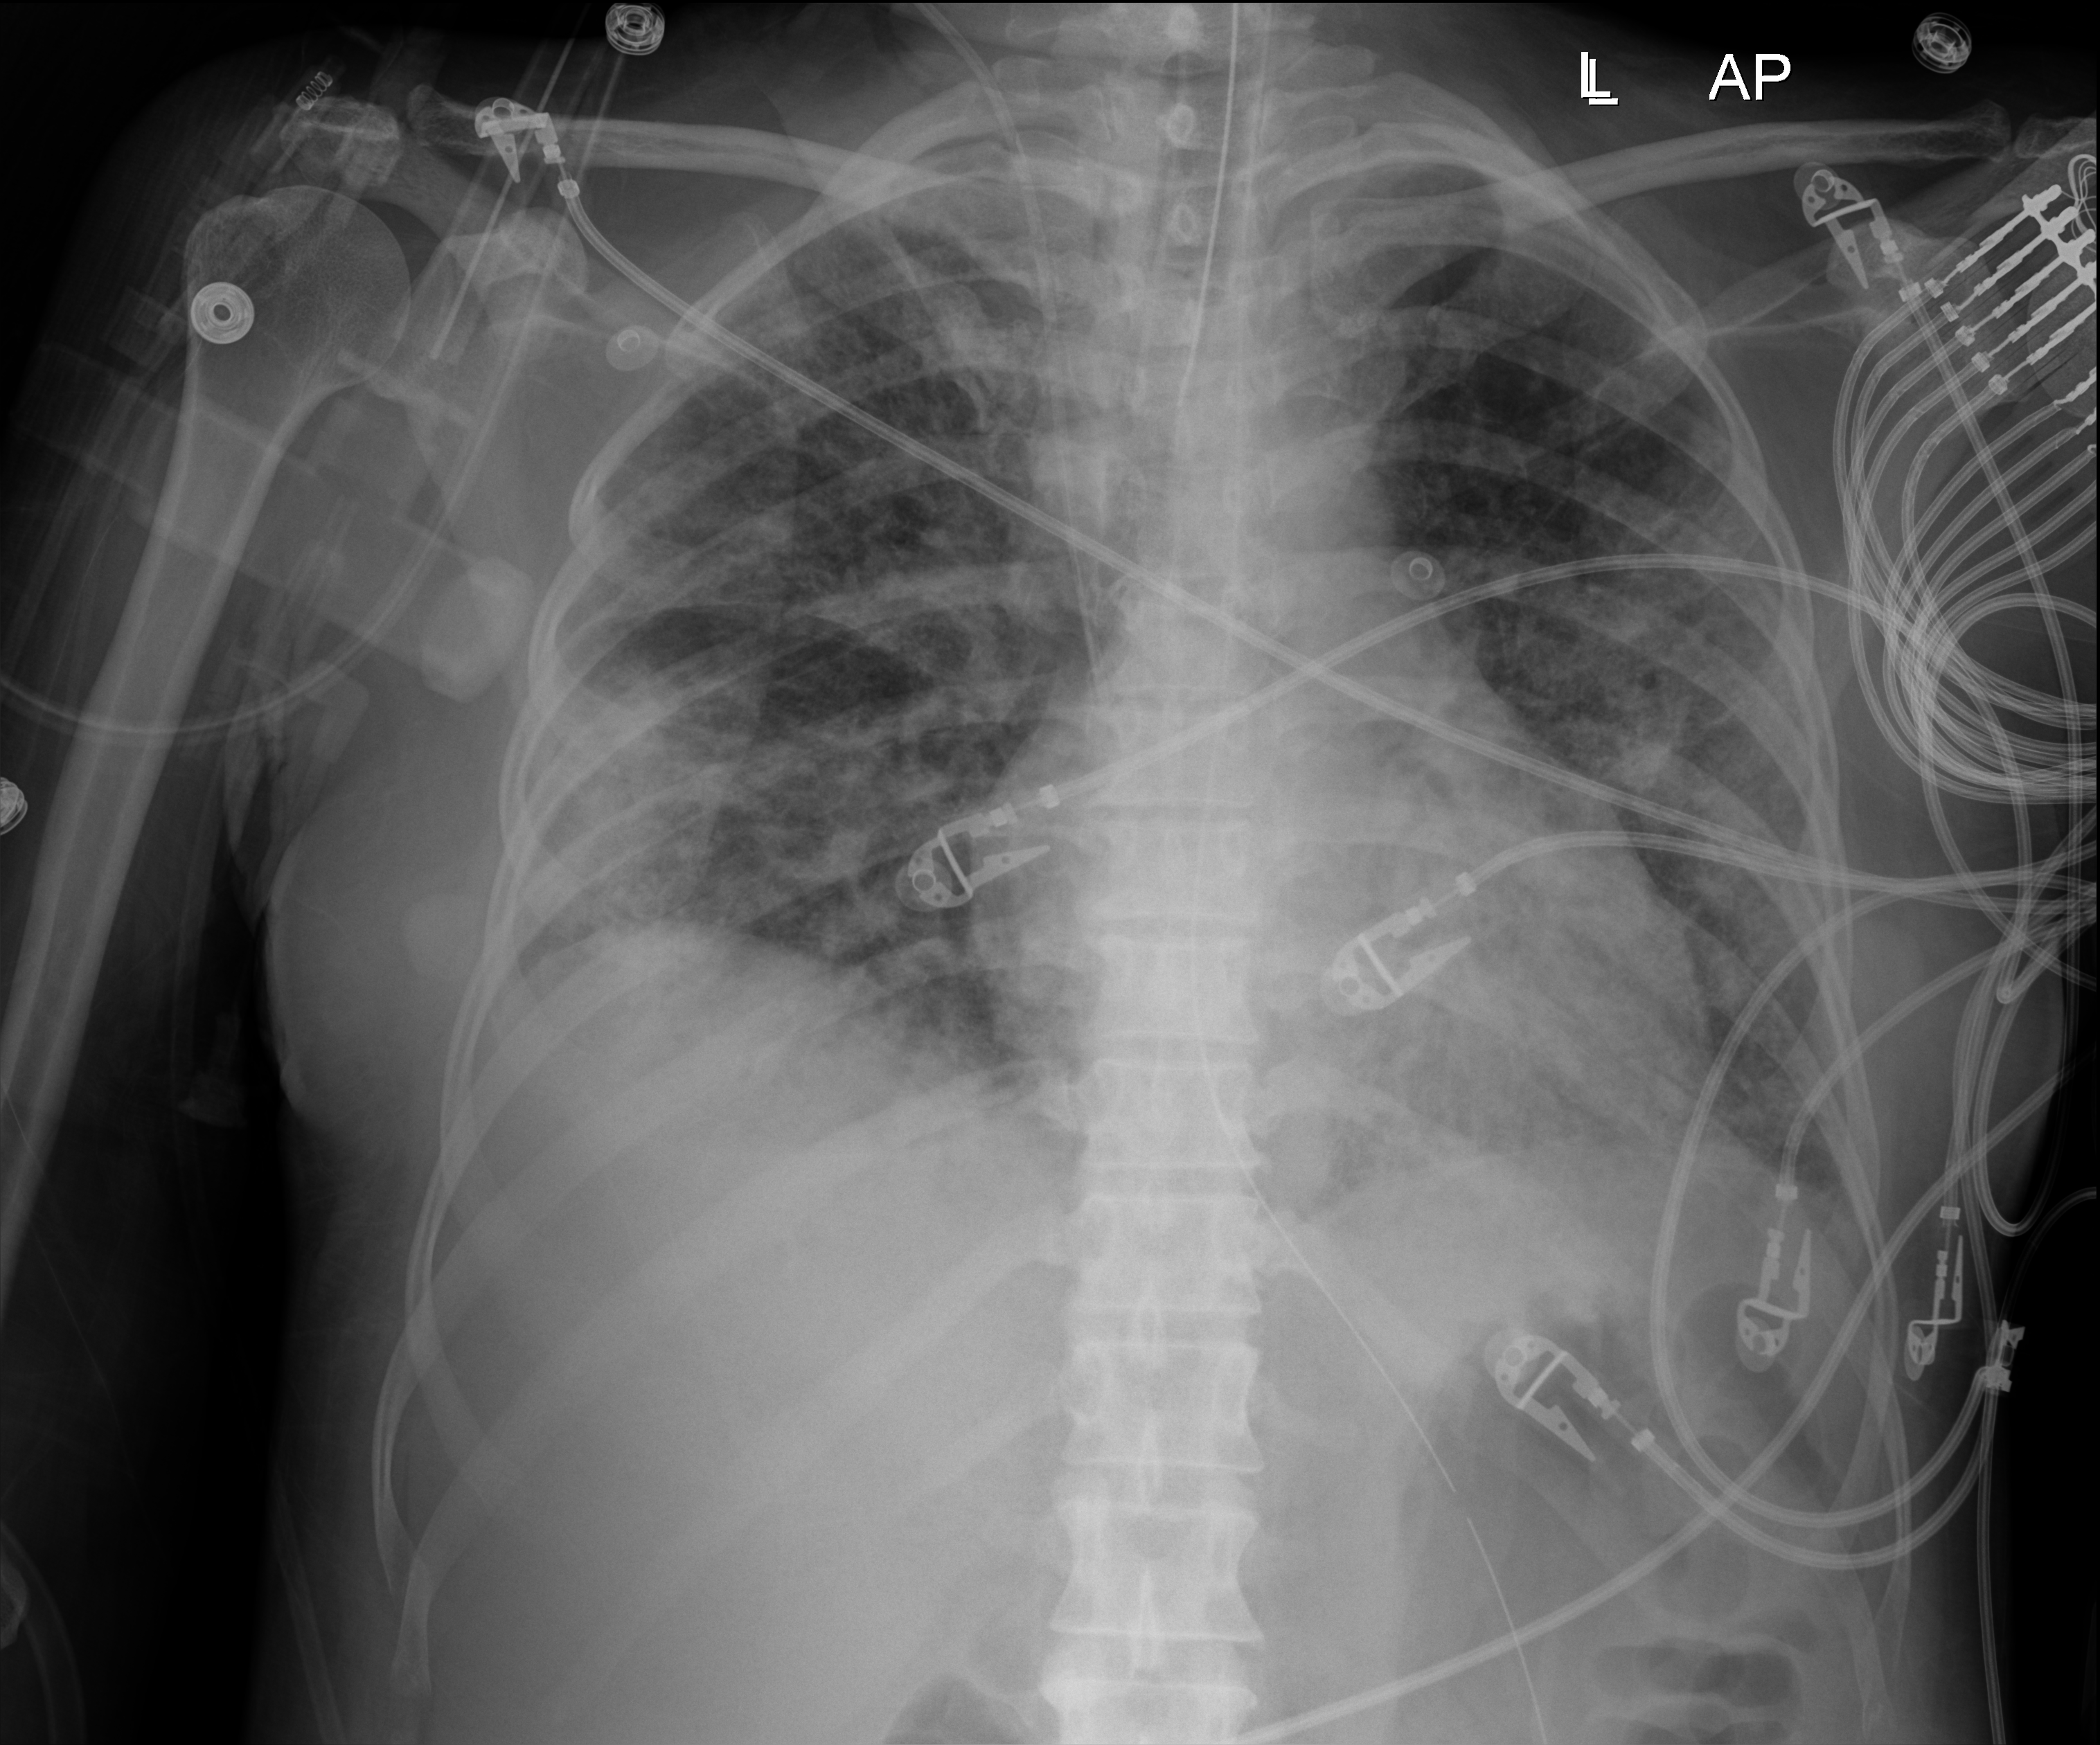
Chest X-ray (portable). Female patient hospitalised with COVID-19, age 18–59 years.
Hospital-stay facts (about this admission, not read from this image; timing relative to this image not recorded): admitted to intensive care during this hospital stay: yes; mechanically ventilated during this hospital stay: yes.